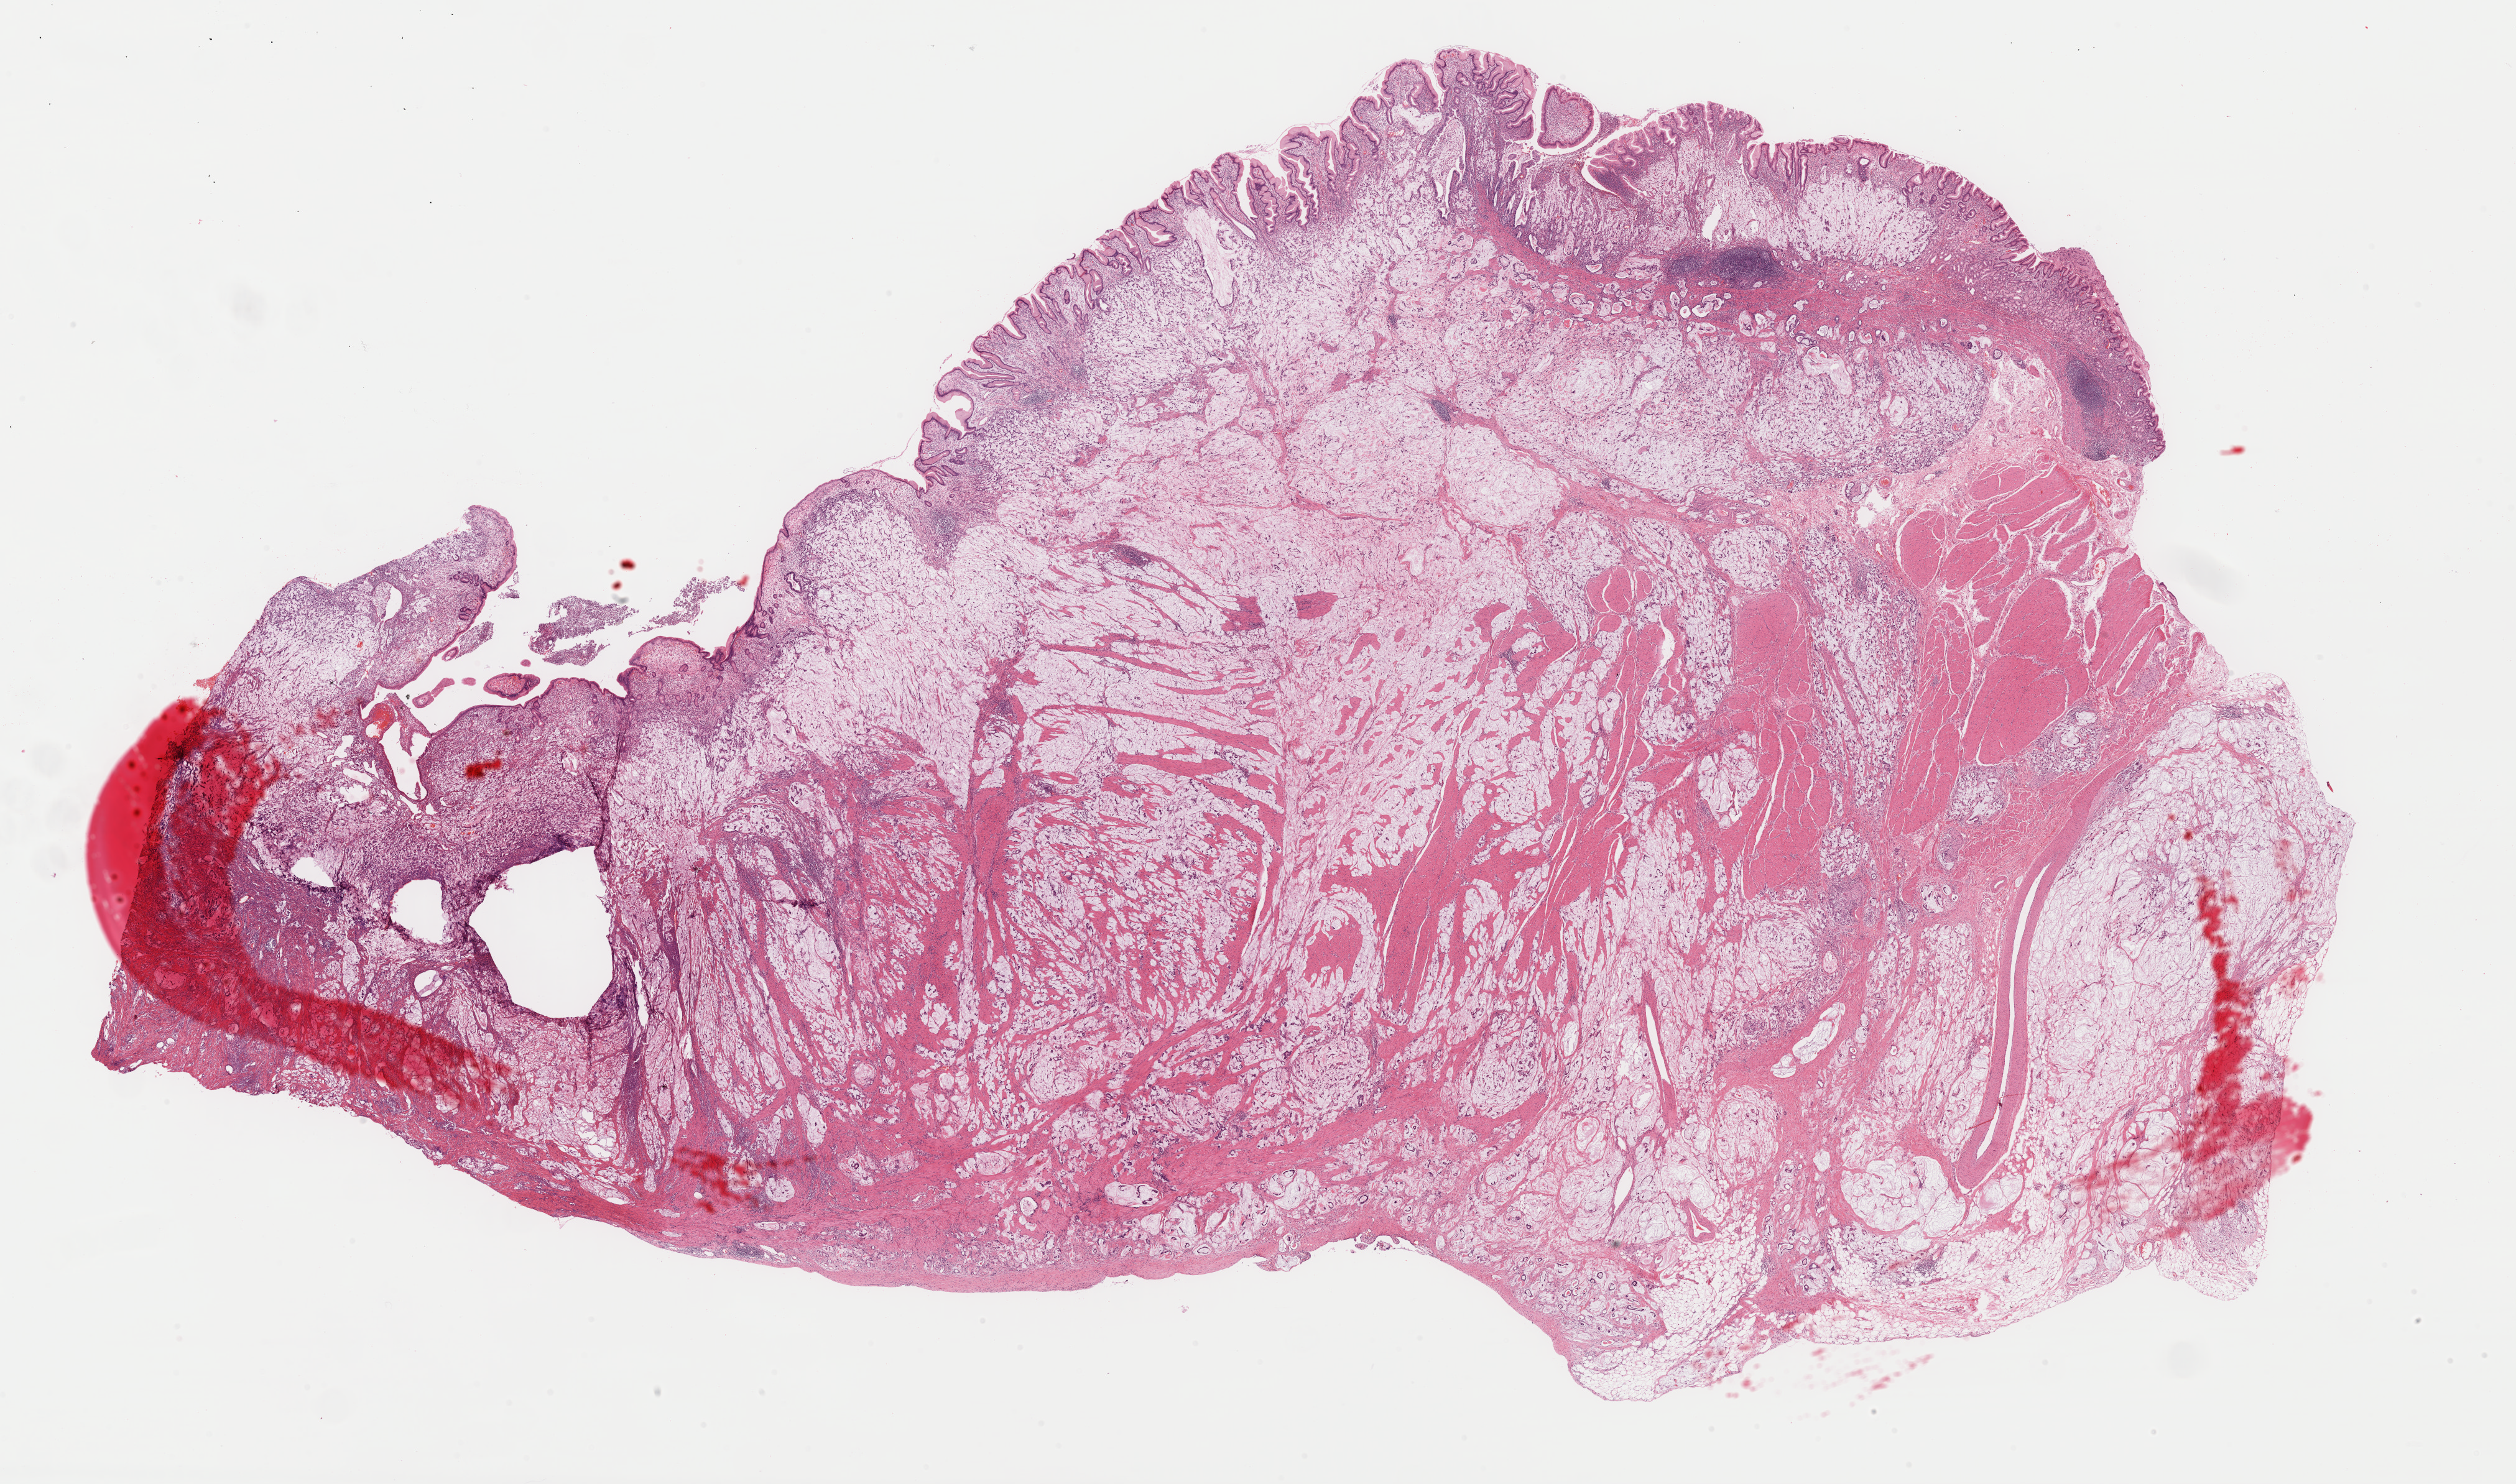
Whole-slide histology image, Hematoxylin and eosin (H&E) stained — whole scanned area (about 32.0 x 18.9 mm) shown as a low-resolution overview, FFPE section, stomach, primary tumour sample. Patient: male, age at initial diagnosis 49 years.
Histologic diagnosis: Mucinous adenocarcinoma (gastric antrum).